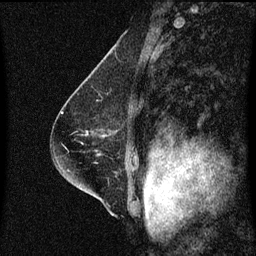
Breast MRI (dynamic contrast-enhanced), one sagittal slice. Dynamic contrast-enhanced series, image 2 of 3 at this slice position (ordered by acquisition). 1.5 T. TE 4.2 ms, TR 8.4 ms. 256 × 256 image matrix. Female patient, age 58 years.
Structures marked on this image (semi-automatic segmentation, software-assisted and operator-edited):
- analysis volume of interest (the breast-tissue region the enhancement analysis was run in; not a lesion): box from (x=86, y=124) to (x=124, y=139) px
- tumour enhancement mask (voxels above the 70 % enhancement threshold inside the analysis volume of interest): (x=86, y=132)–(x=88, y=135)